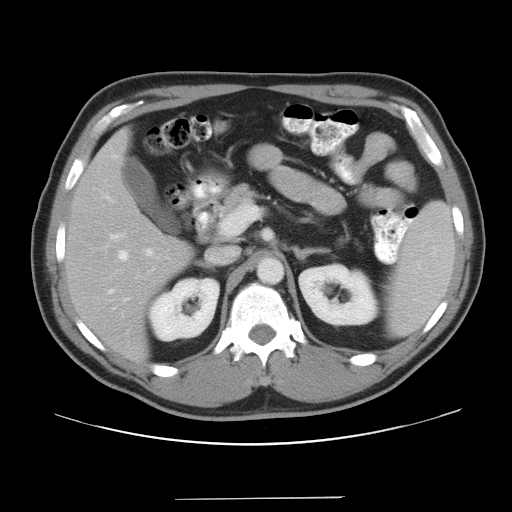
Contrast-enhanced abdominal CT, one axial slice; slice 22 of 37 in the series (ordered by position); reconstruction kernel STANDARD; intravenous contrast given; soft-tissue window (W 400 / L 40 HU); 7.5 mm slice thickness; 512 × 512 image matrix, field of view 400 × 400 mm. Male patient, age 46 years. From the clinical record (not read from this slice): diagnosis: colorectal cancer liver metastases, imaged before liver resection; multiple liver metastases: yes; largest metastasis: 1 cm; chemotherapy before resection: yes.
Outlined on this slice (outlined manually by an expert reader):
- hepatic veins: bounding box [x1, y1, x2, y2] px = [108, 235, 128, 294]
- liver: [67, 133, 189, 356]
- planned liver remnant (the part of the liver to remain after resection): [67, 133, 189, 357]
- portal vein (with intrahepatic branches): [146, 249, 152, 256]